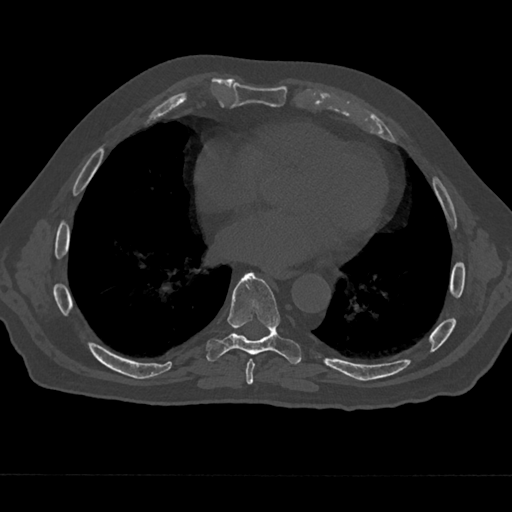
CT including the spine, one axial slice. Reconstruction kernel Br40s/3. Bone window (W 1800 / L 400 HU). 0.5 mm slice thickness. 512 × 512 image matrix, field of view 377 × 377 mm. Male patient, age 75 years. Case-level facts recorded for this patient, not image findings: primary cancer: renal; vertebrae with lytic lesions (as recorded): T4.
Annotated regions visible in this slice (semi-automatically segmented with operator editing):
- T7 vertebra: bounding box [x1, y1, x2, y2] px = [243, 358, 257, 385]
- T8 vertebra: [206, 272, 301, 365]